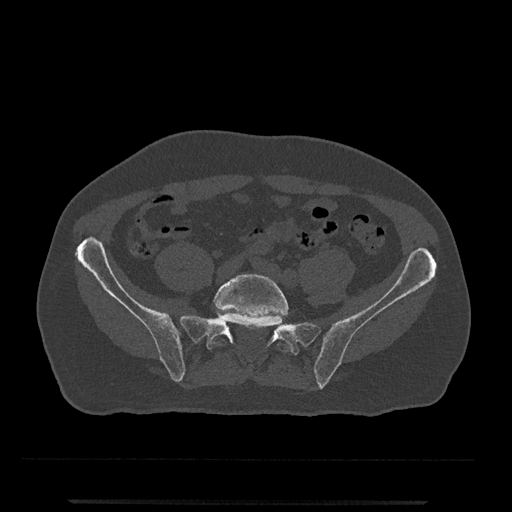
CT including the spine, one axial slice; slice 41 of 797 in the series (ordered by position); reconstruction kernel Br40s/3; 120 kVp; bone window (W 1800 / L 400 HU); 0.5 mm slice thickness; 512 × 512 image matrix. Patient: male, 63 years. Case-level facts recorded for this patient, not image findings: primary cancer: prostate.
Structures marked on this image (semi-automatic segmentation, software-assisted and operator-edited):
- L5 vertebra: box from (x=209, y=274) to (x=289, y=352) px